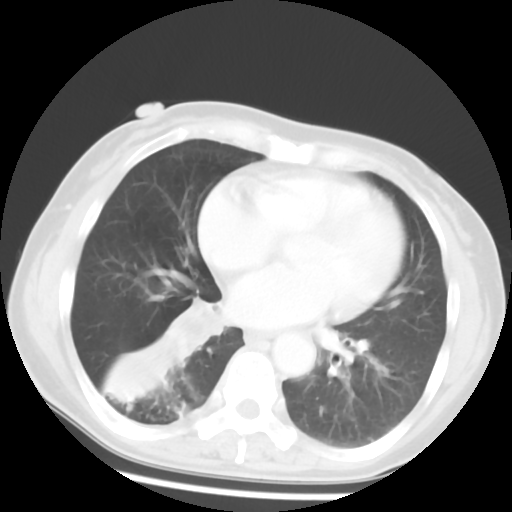
Chest CT, one axial slice; slice 23 of 52 in the series (ordered by position); reconstruction kernel STANDARD; 120 kVp; lung window (W 1500 / L -600 HU); 5 mm slice thickness; 512 × 512 image matrix. Female patient, age 54 years. Case-level facts recorded for this patient, not image findings: clinical TNM (as recorded): T1c N0 M0; histopathological grade: G1-2.
Annotated regions visible in this slice (bounding box drawn by a radiologist):
- lung tumour (recorded histology: squamous cell carcinoma): bounding box (x1, y1, x2, y2) in pixels: (166, 284, 224, 362)